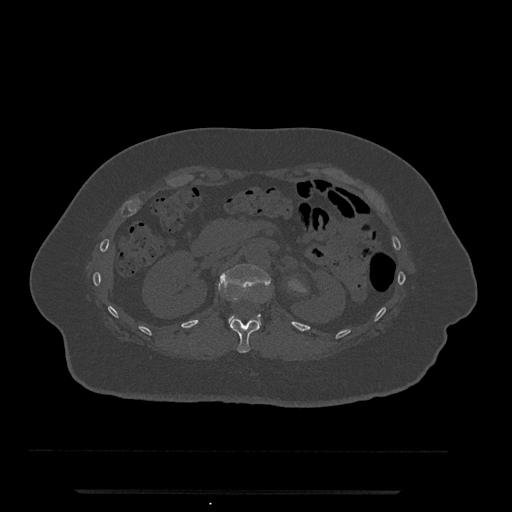
CT including the spine, one axial slice. Slice 139 of 797 in the series (ordered by position). Bone window (W 1800 / L 400 HU). 0.5 mm slice thickness. 512 × 512 image matrix, field of view 440 × 440 mm. Patient: female, 51 years. Case-level facts recorded for this patient, not image findings: primary cancer: neuro.
Outlined on this slice (semi-automatic segmentation, software-assisted and operator-edited):
- L1 vertebra: box from (x=218, y=264) to (x=271, y=328) px
- T12 vertebra: (x=230, y=318)–(x=259, y=353)